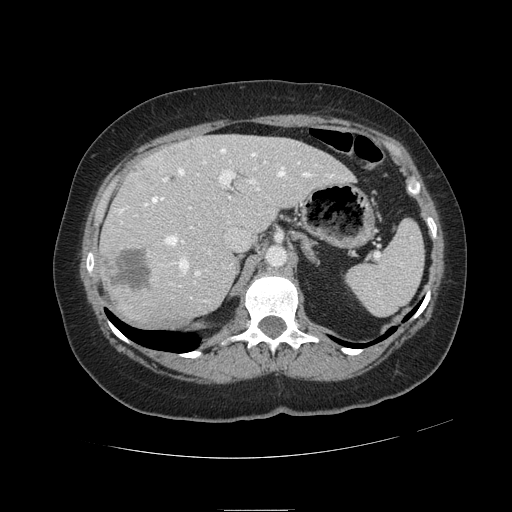
Contrast-enhanced abdominal CT, one axial slice; position 74 of 121 along the scan axis; 120 kVp; intravenous contrast given; soft-tissue window (W 400 / L 40 HU); 512 × 512 image matrix, field of view 400 × 400 mm. Female patient, age 52 years. From the clinical record (not read from this slice): diagnosis: colorectal cancer liver metastases, imaged before liver resection; multiple liver metastases: yes.
Outlined on this slice (manually delineated by an expert):
- hepatic veins: bounding box <118,149,334,299> (left, top, right, bottom; pixels)
- liver: <101,136,352,324>
- planned liver remnant (the part of the liver to remain after resection): <167,135,352,232>
- portal vein (with intrahepatic branches): <121,161,266,283>
- liver metastasis: <111,245,152,291>